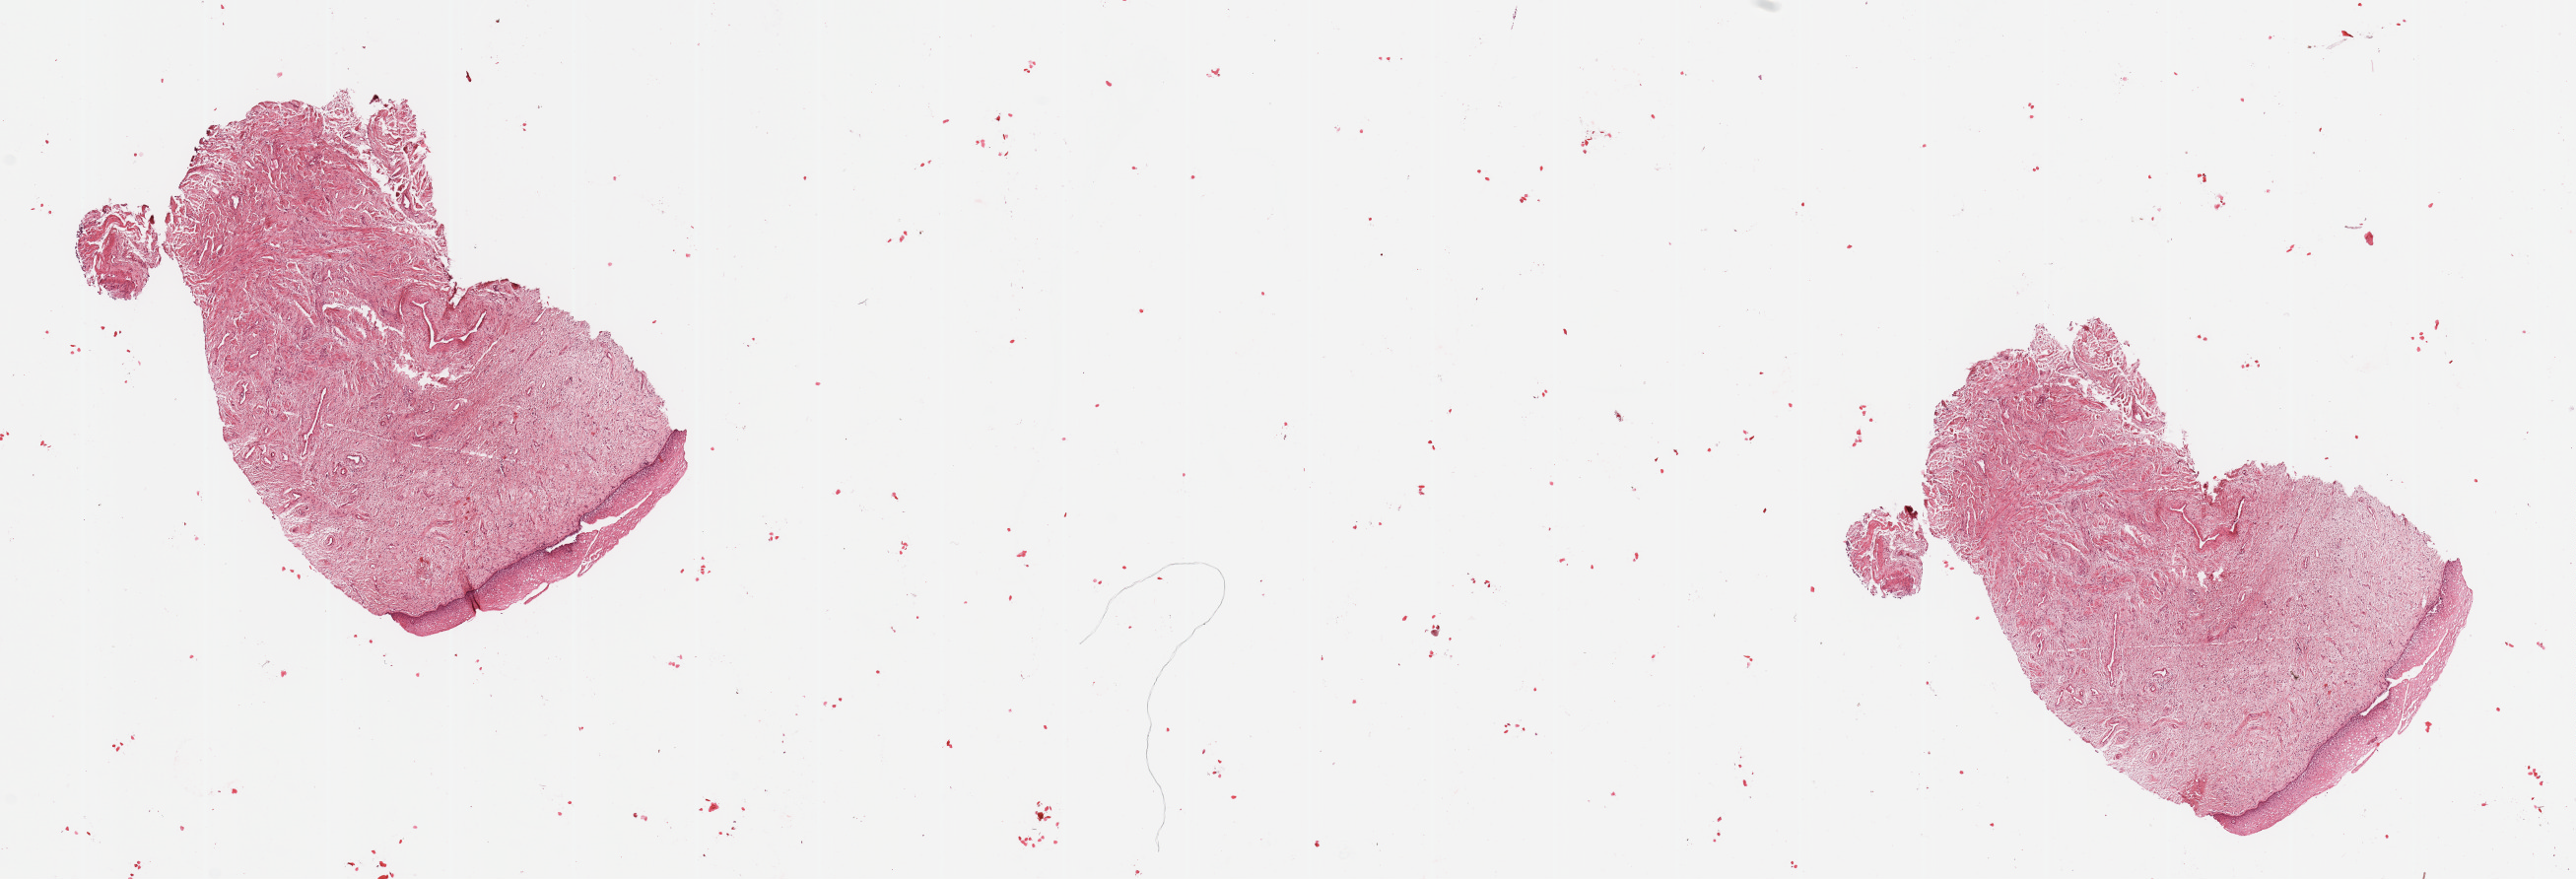
Digitized H&E-stained tissue section (whole slide), low-resolution overview of the scanned area, about 20.7 x 7.1 mm (acquisition: 20x scan), normal (non-tumour) tissue sample, uterus. Female, 72 y/o.
This section: normal (non-tumour) tissue from the same patient. Patient diagnosis (cohort enrolment): corpus endometrial carcinoma (uterus).